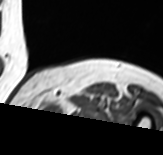
MRI of an extremity soft-tissue mass, one axial slice. Position 56 of 65 along the scan axis. MR volume resampled by the dataset authors to the PET/CT grid (not the native acquisition matrix). 163 × 155 image matrix. Female patient. Case-level facts recorded for this patient, not image findings: histological type: pleomorphic leiomyosarcoma; grade: high; site of the primary tumour: left thigh.
Outlined on this slice (expert contour drawn on MRI and transferred to this co-registered scan by the dataset authors):
- gross tumour volume including surrounding oedema: bounding box [x1, y1, x2, y2] px = [42, 101, 65, 123]